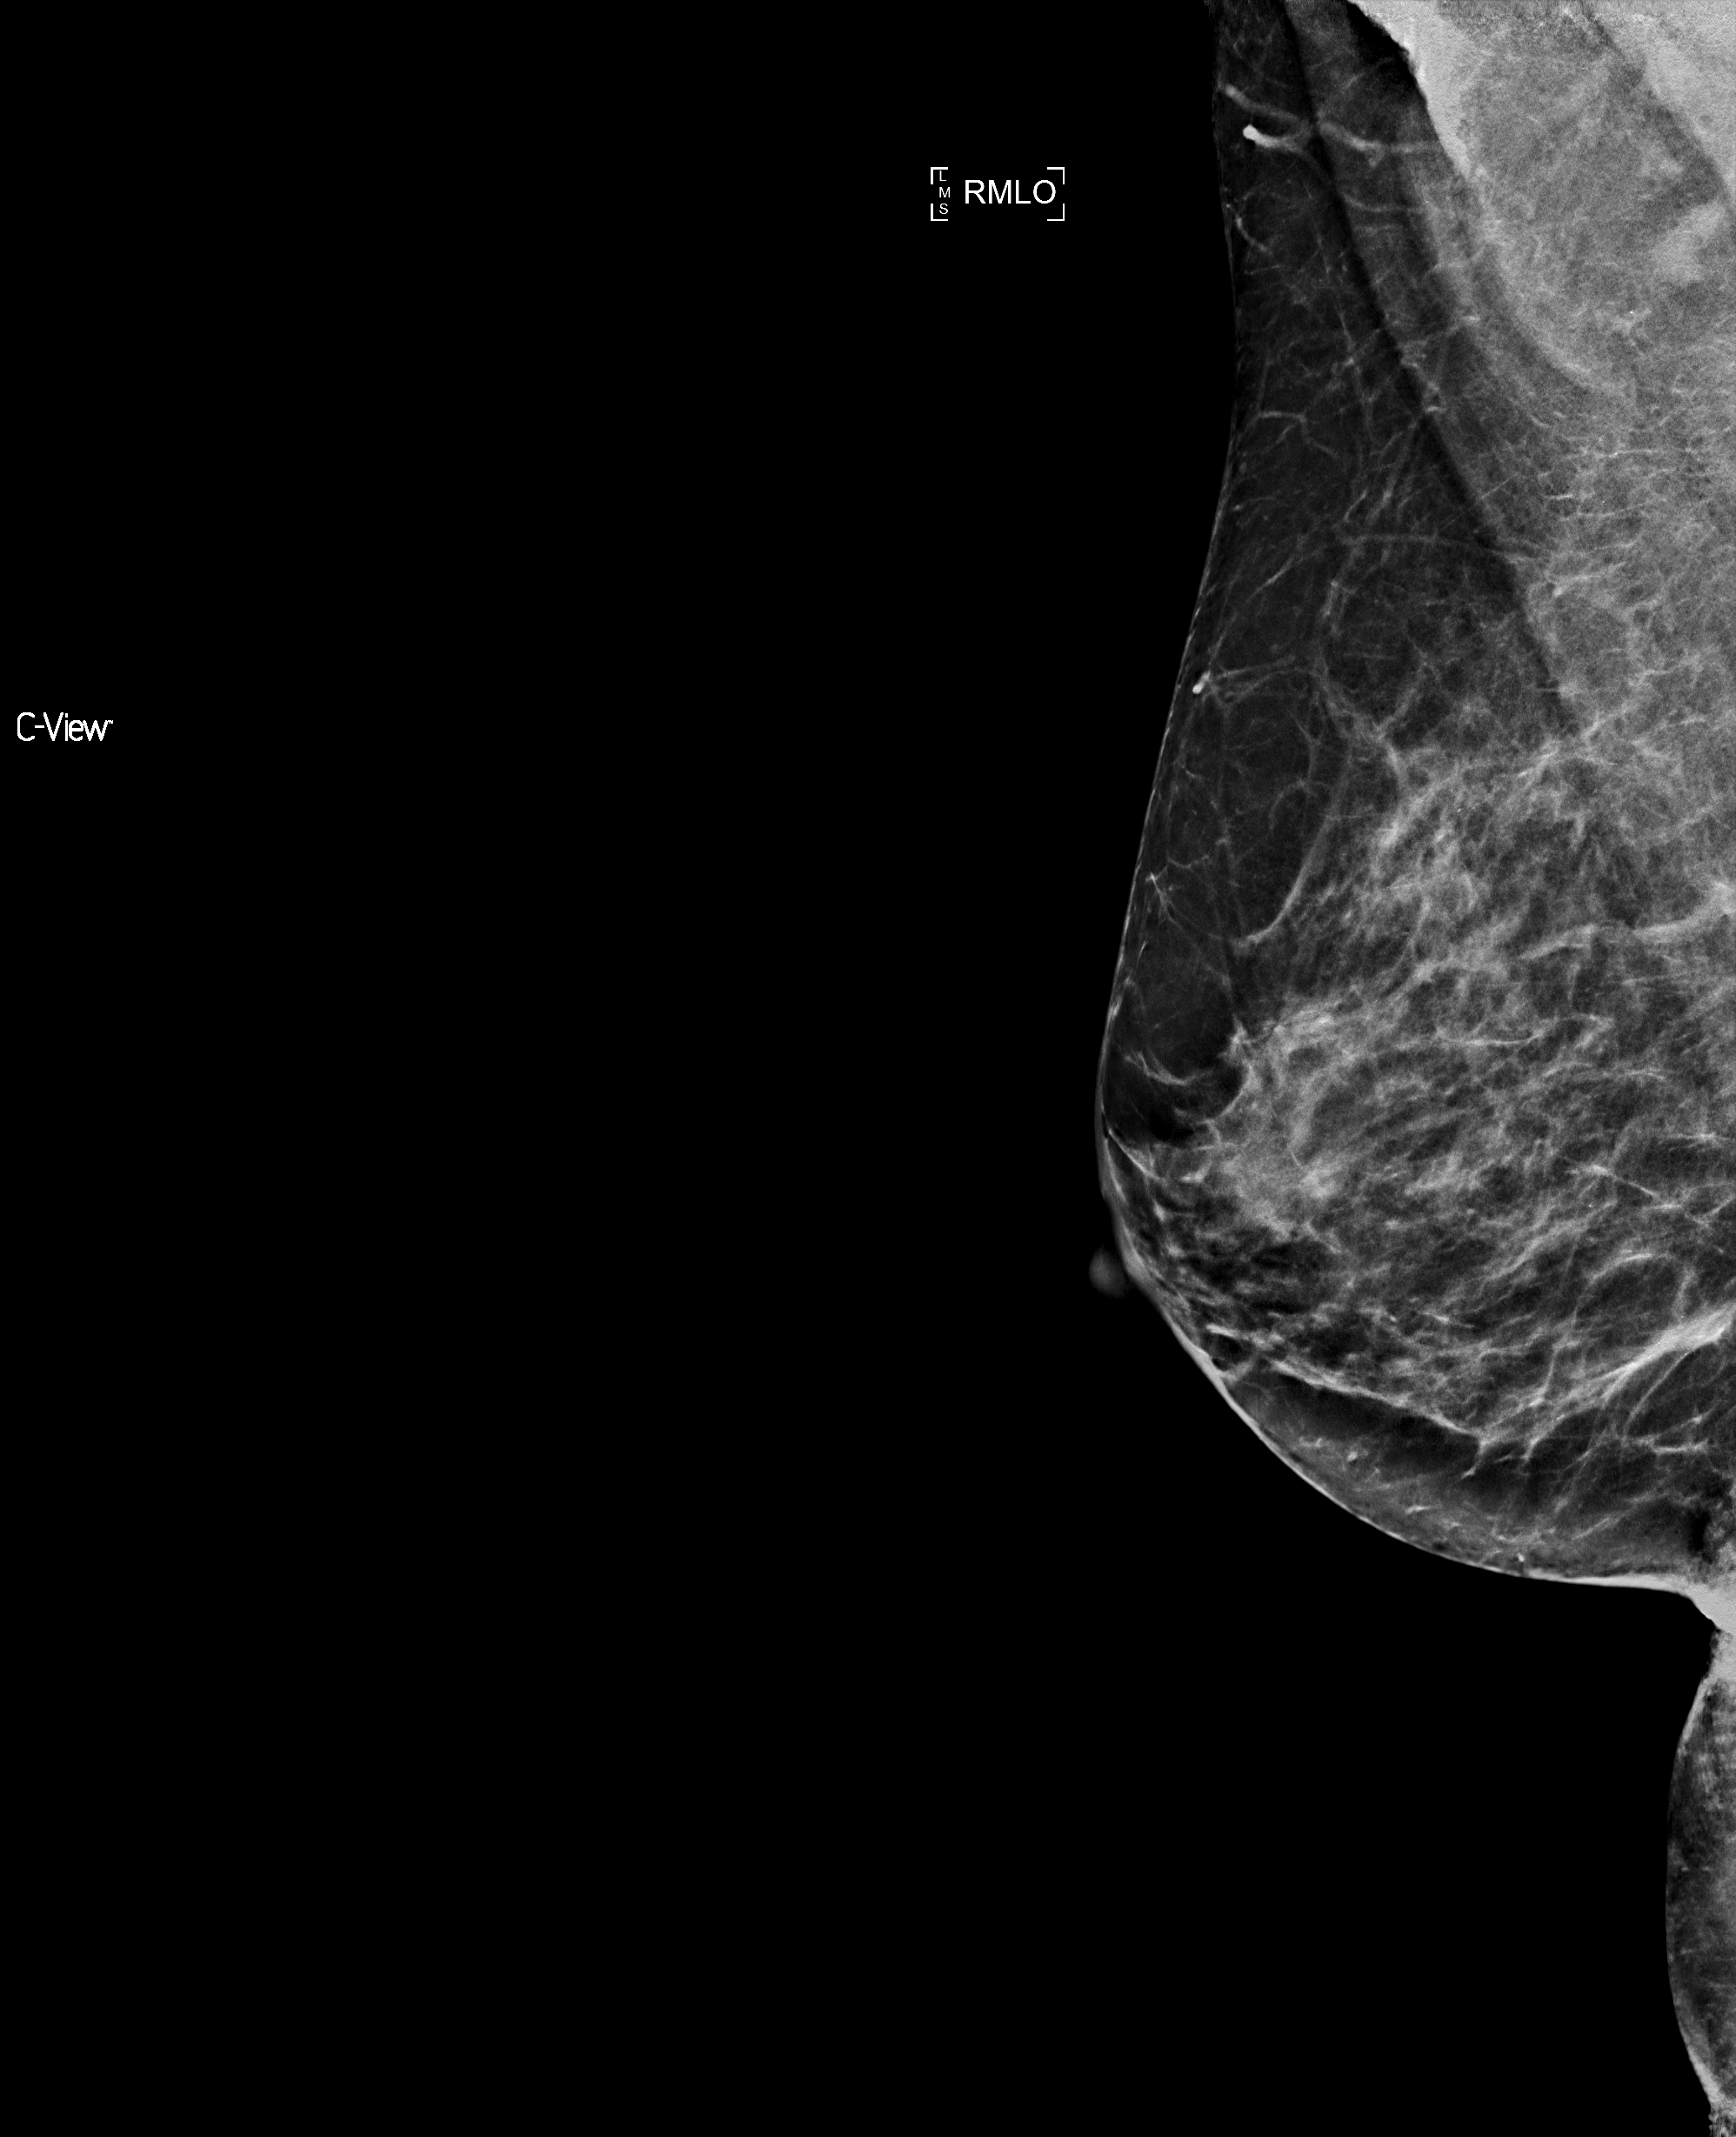
Full-field digital mammogram (FFDM), right breast, MLO view, annual screening mammography examination, compressed breast thickness 57 mm, system: Selenia Dimensions. Patient aged 59 years (female).
BI-RADS breast density category at the screening exam (both breasts, scale 1–4): 3. Final BI-RADS category for the screening round (tomosynthesis exam, both breasts): category 1. Recall: no recall after this screen.